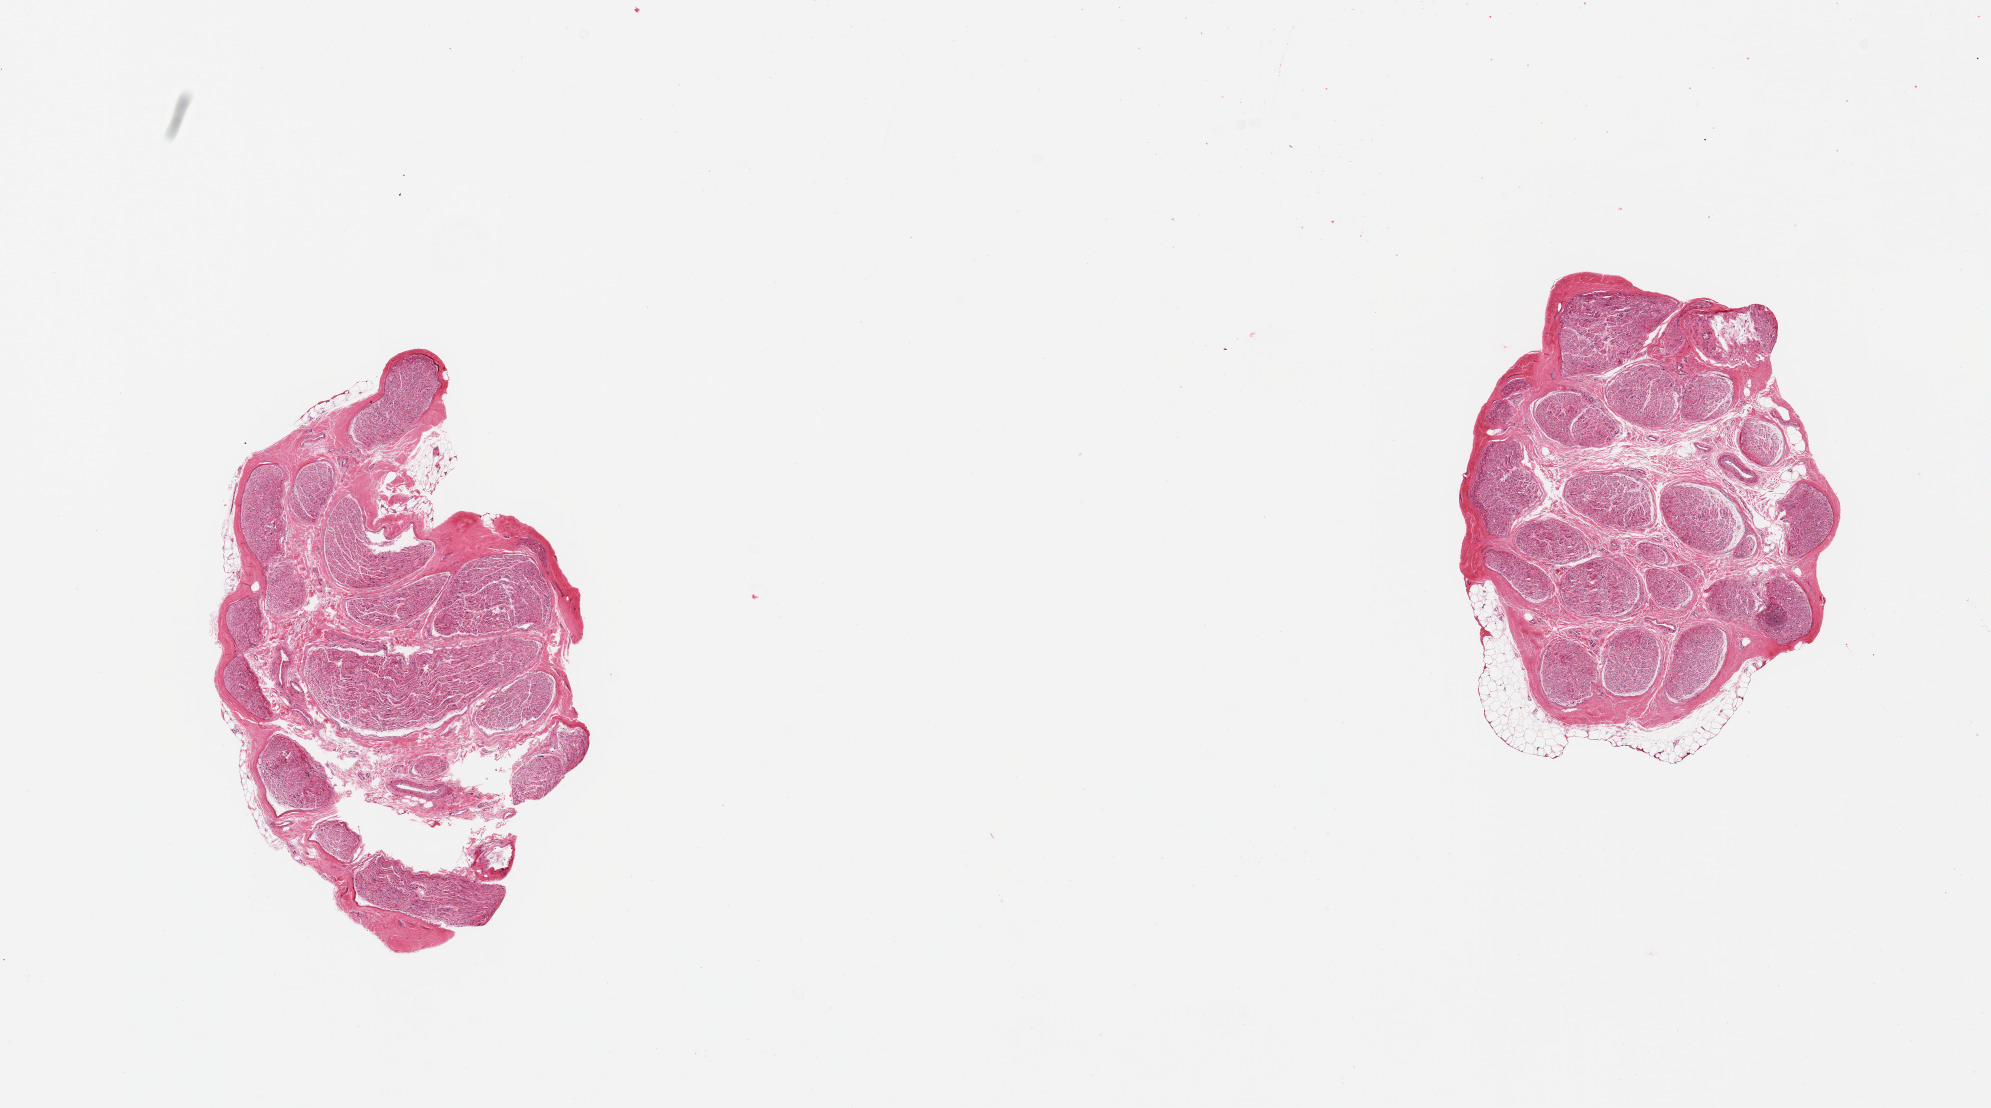
Whole-slide image, hematoxylin and eosin (H&E) stain — a low-resolution overview of the entire scanned area, about 15.8 x 8.8 mm, PAXgene-fixed, paraffin-embedded tissue, sampled site (target tissue): tibial nerve, donor tissue sample. Donor sex: male.
Pathologist's review note for this sample: 2 pieces; nerve with minimal attachment of fat.